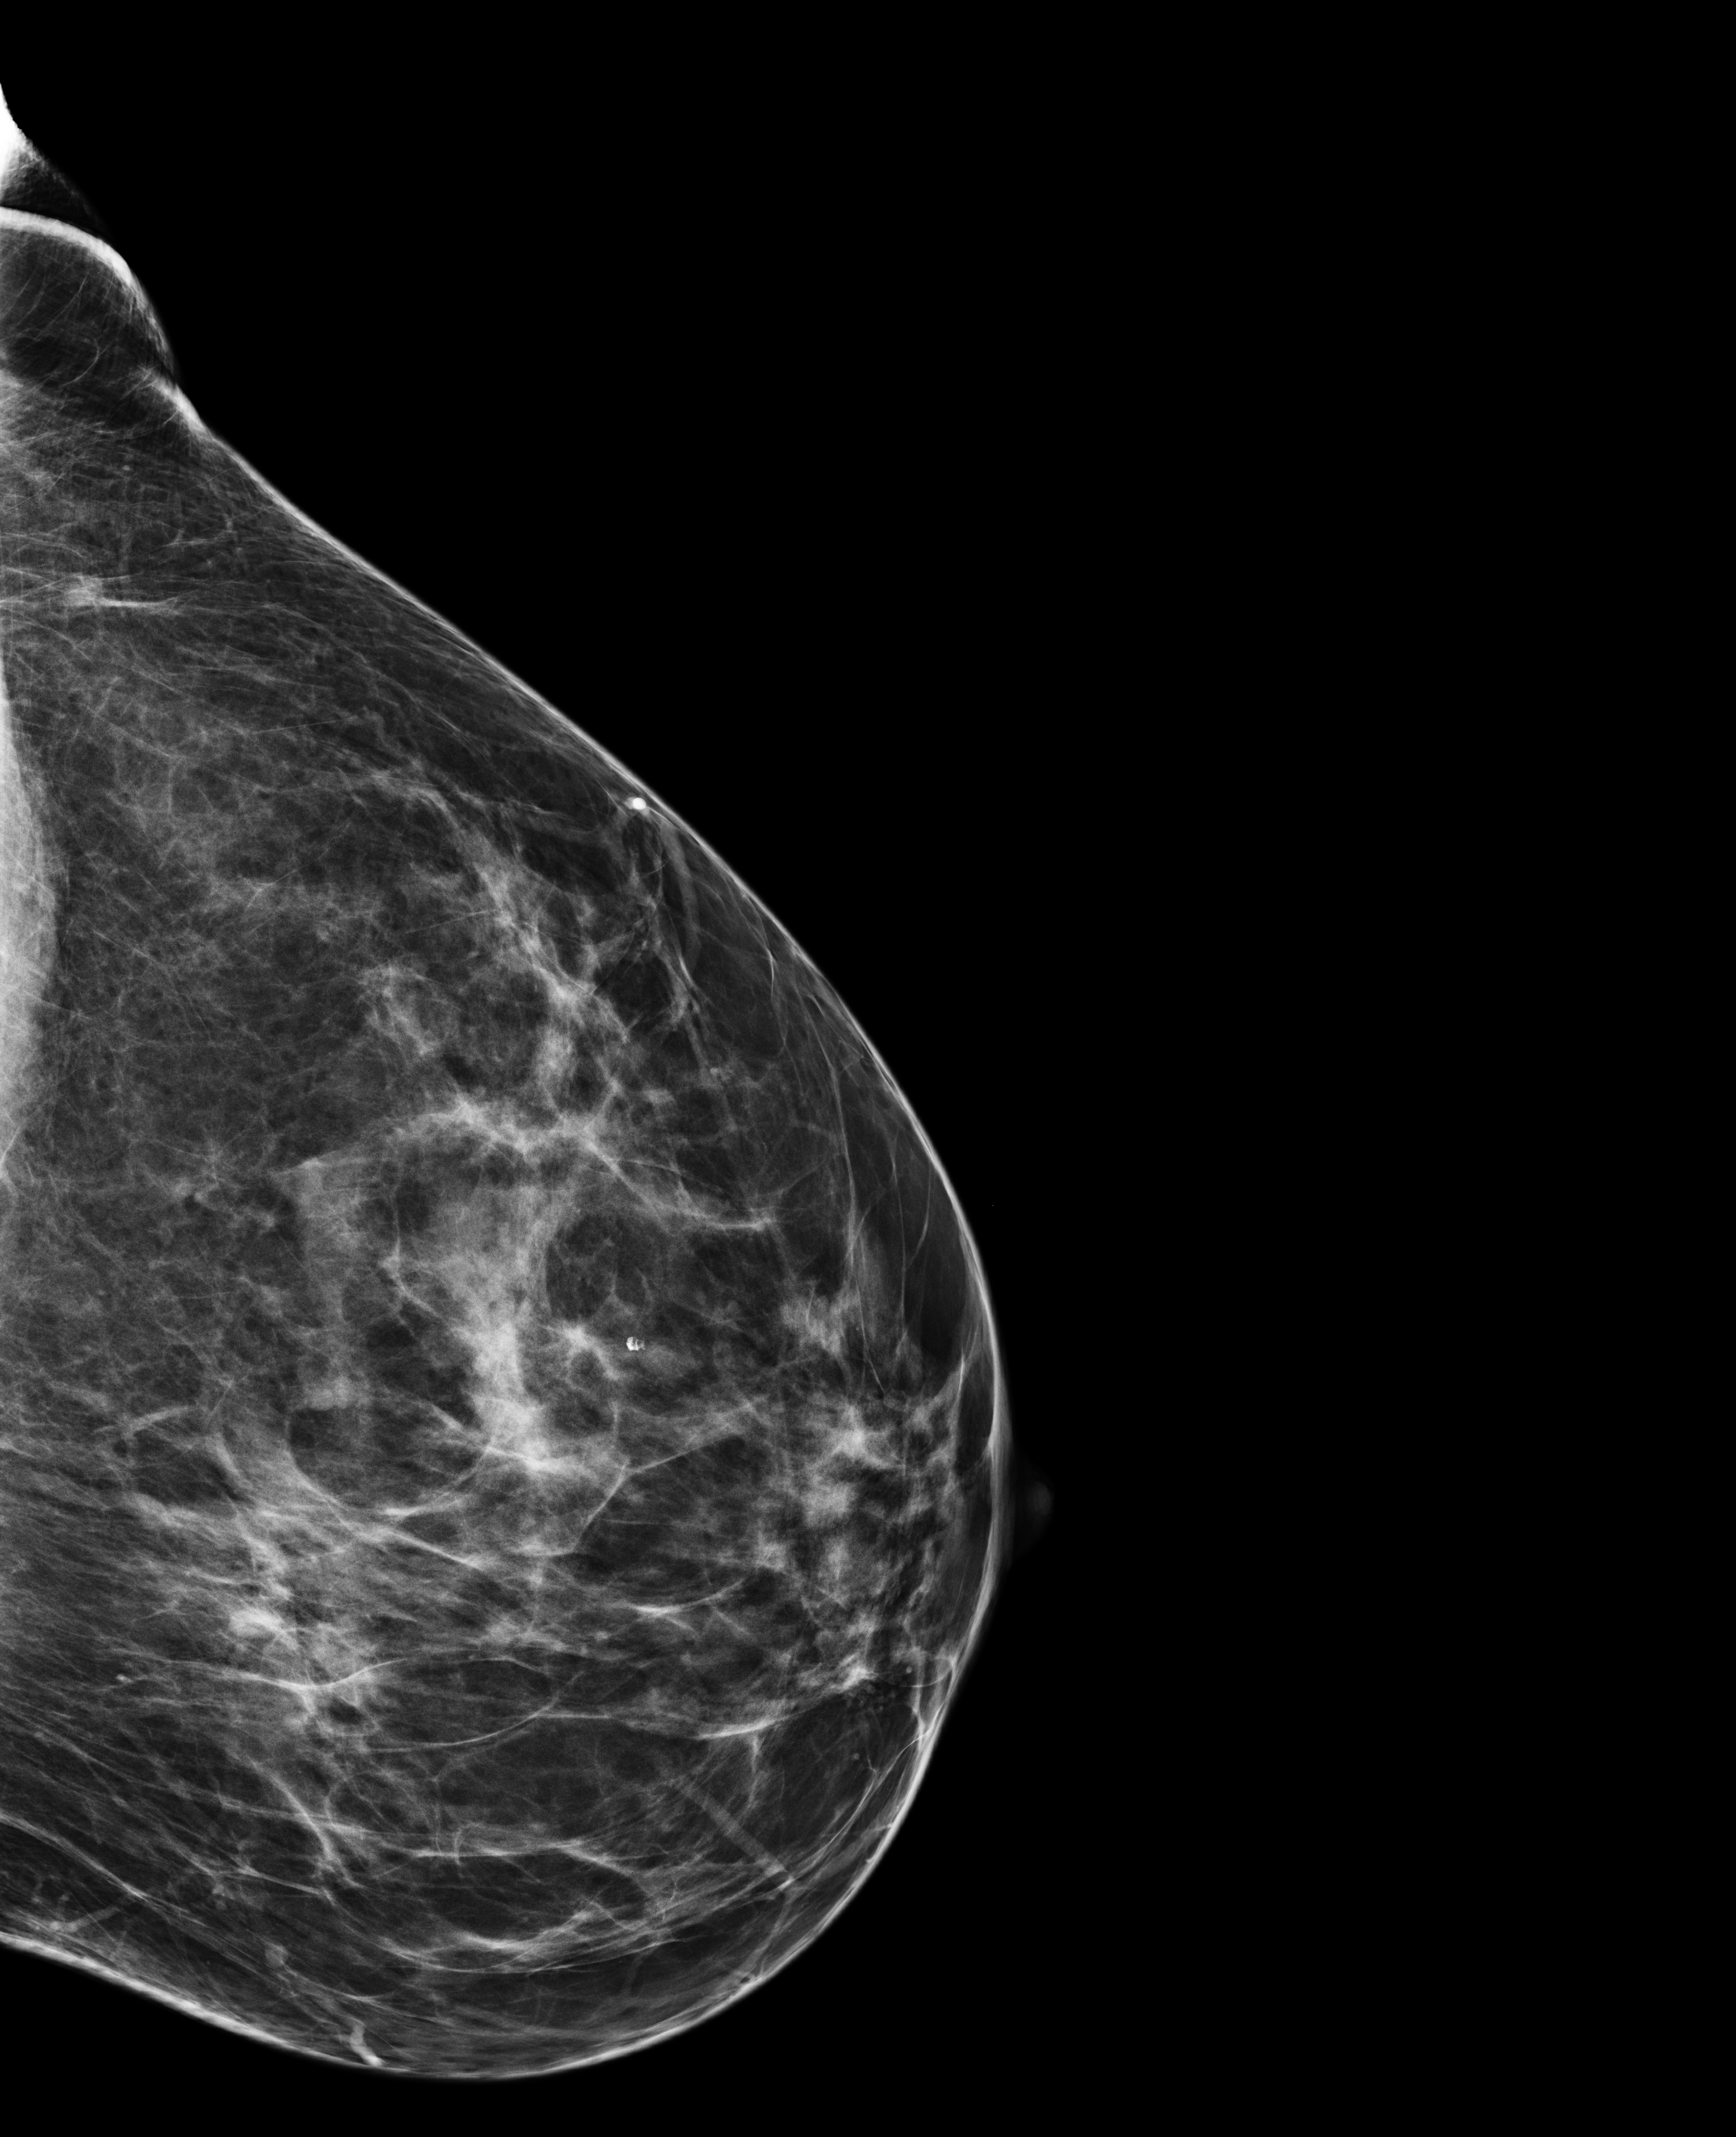
Digital mammogram (FFDM), left breast, laterally exaggerated craniocaudal (XCCL) view, screening examination, compressed breast thickness 75 mm, system: Selenia Dimensions. Patient: female, 47 years.
BI-RADS breast density category at the screening exam (both breasts, scale 1–4): 3. Final BI-RADS assessment for this screening round (tomosynthesis exam, both breasts): category 2. Recall: no recall after this screen.